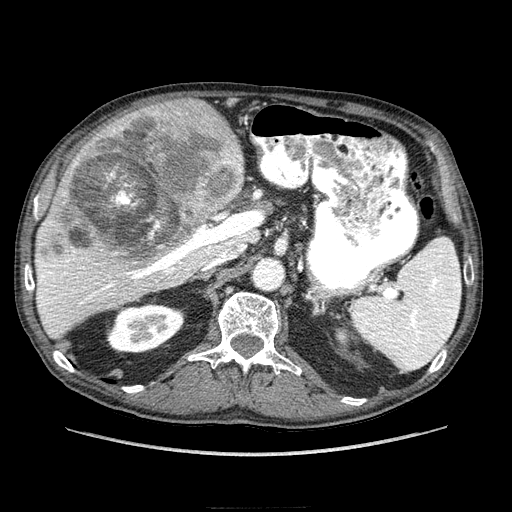
Contrast-enhanced abdominal CT (liver protocol), one axial slice; slice 145 of 218 in the series (ordered by position); 100 kVp; soft-tissue window (W 400 / L 40 HU); 512 × 512 image matrix. Case-level facts recorded for this patient, not image findings: diagnosis: hepatocellular carcinoma (patient treated with transarterial chemoembolisation; whether this scan precedes or follows treatment is not stated here); TNM stage (as recorded): Stage-IIIA; Child-Pugh class: A.
Structures marked on this image (semi-automatically segmented with operator editing):
- liver parenchyma outside the tumour (the mass and vessels are separate outlines, so this box may not span the whole liver): bounding box <34,106,270,338> (left, top, right, bottom; pixels)
- mass: <37,99,245,274>
- liver vessels: <37,196,263,323>